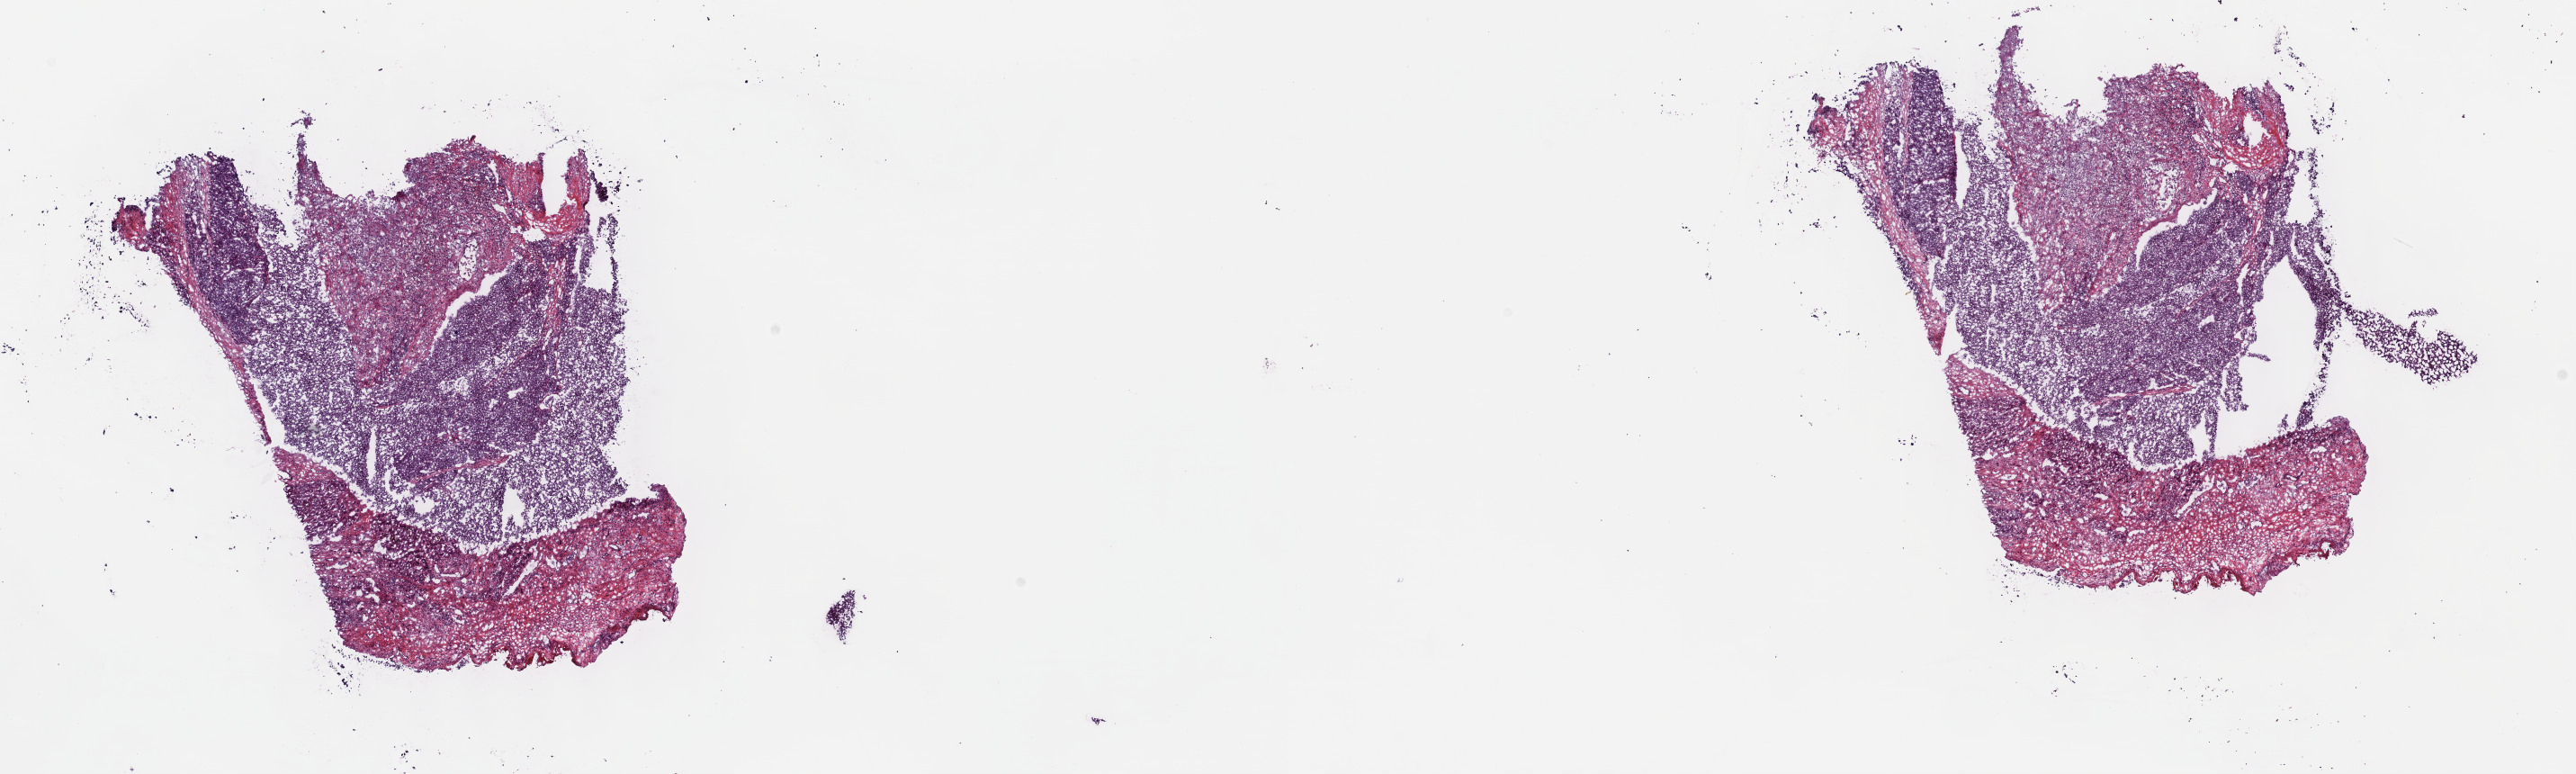
Digitized H&E-stained tissue section (whole slide), shown as a low-resolution overview of the whole scanned area (about 23.2 x 7.0 mm), frozen section from the top of the tissue portion, skin, primary tumour sample. Male, age 58 years at initial diagnosis. Pathologist review of this section (percent, as recorded): tumour cells 100%, tumour nuclei 70%, normal cells 0%, stromal cells 0%, necrosis 0%. Infiltration values recorded for this section: lymphocyte infiltration 2%, monocyte infiltration 0%, neutrophil infiltration 0%.
- histologic diagnosis: Epithelioid cell melanoma
- AJCC pathologic stage: IIC (7th edition)